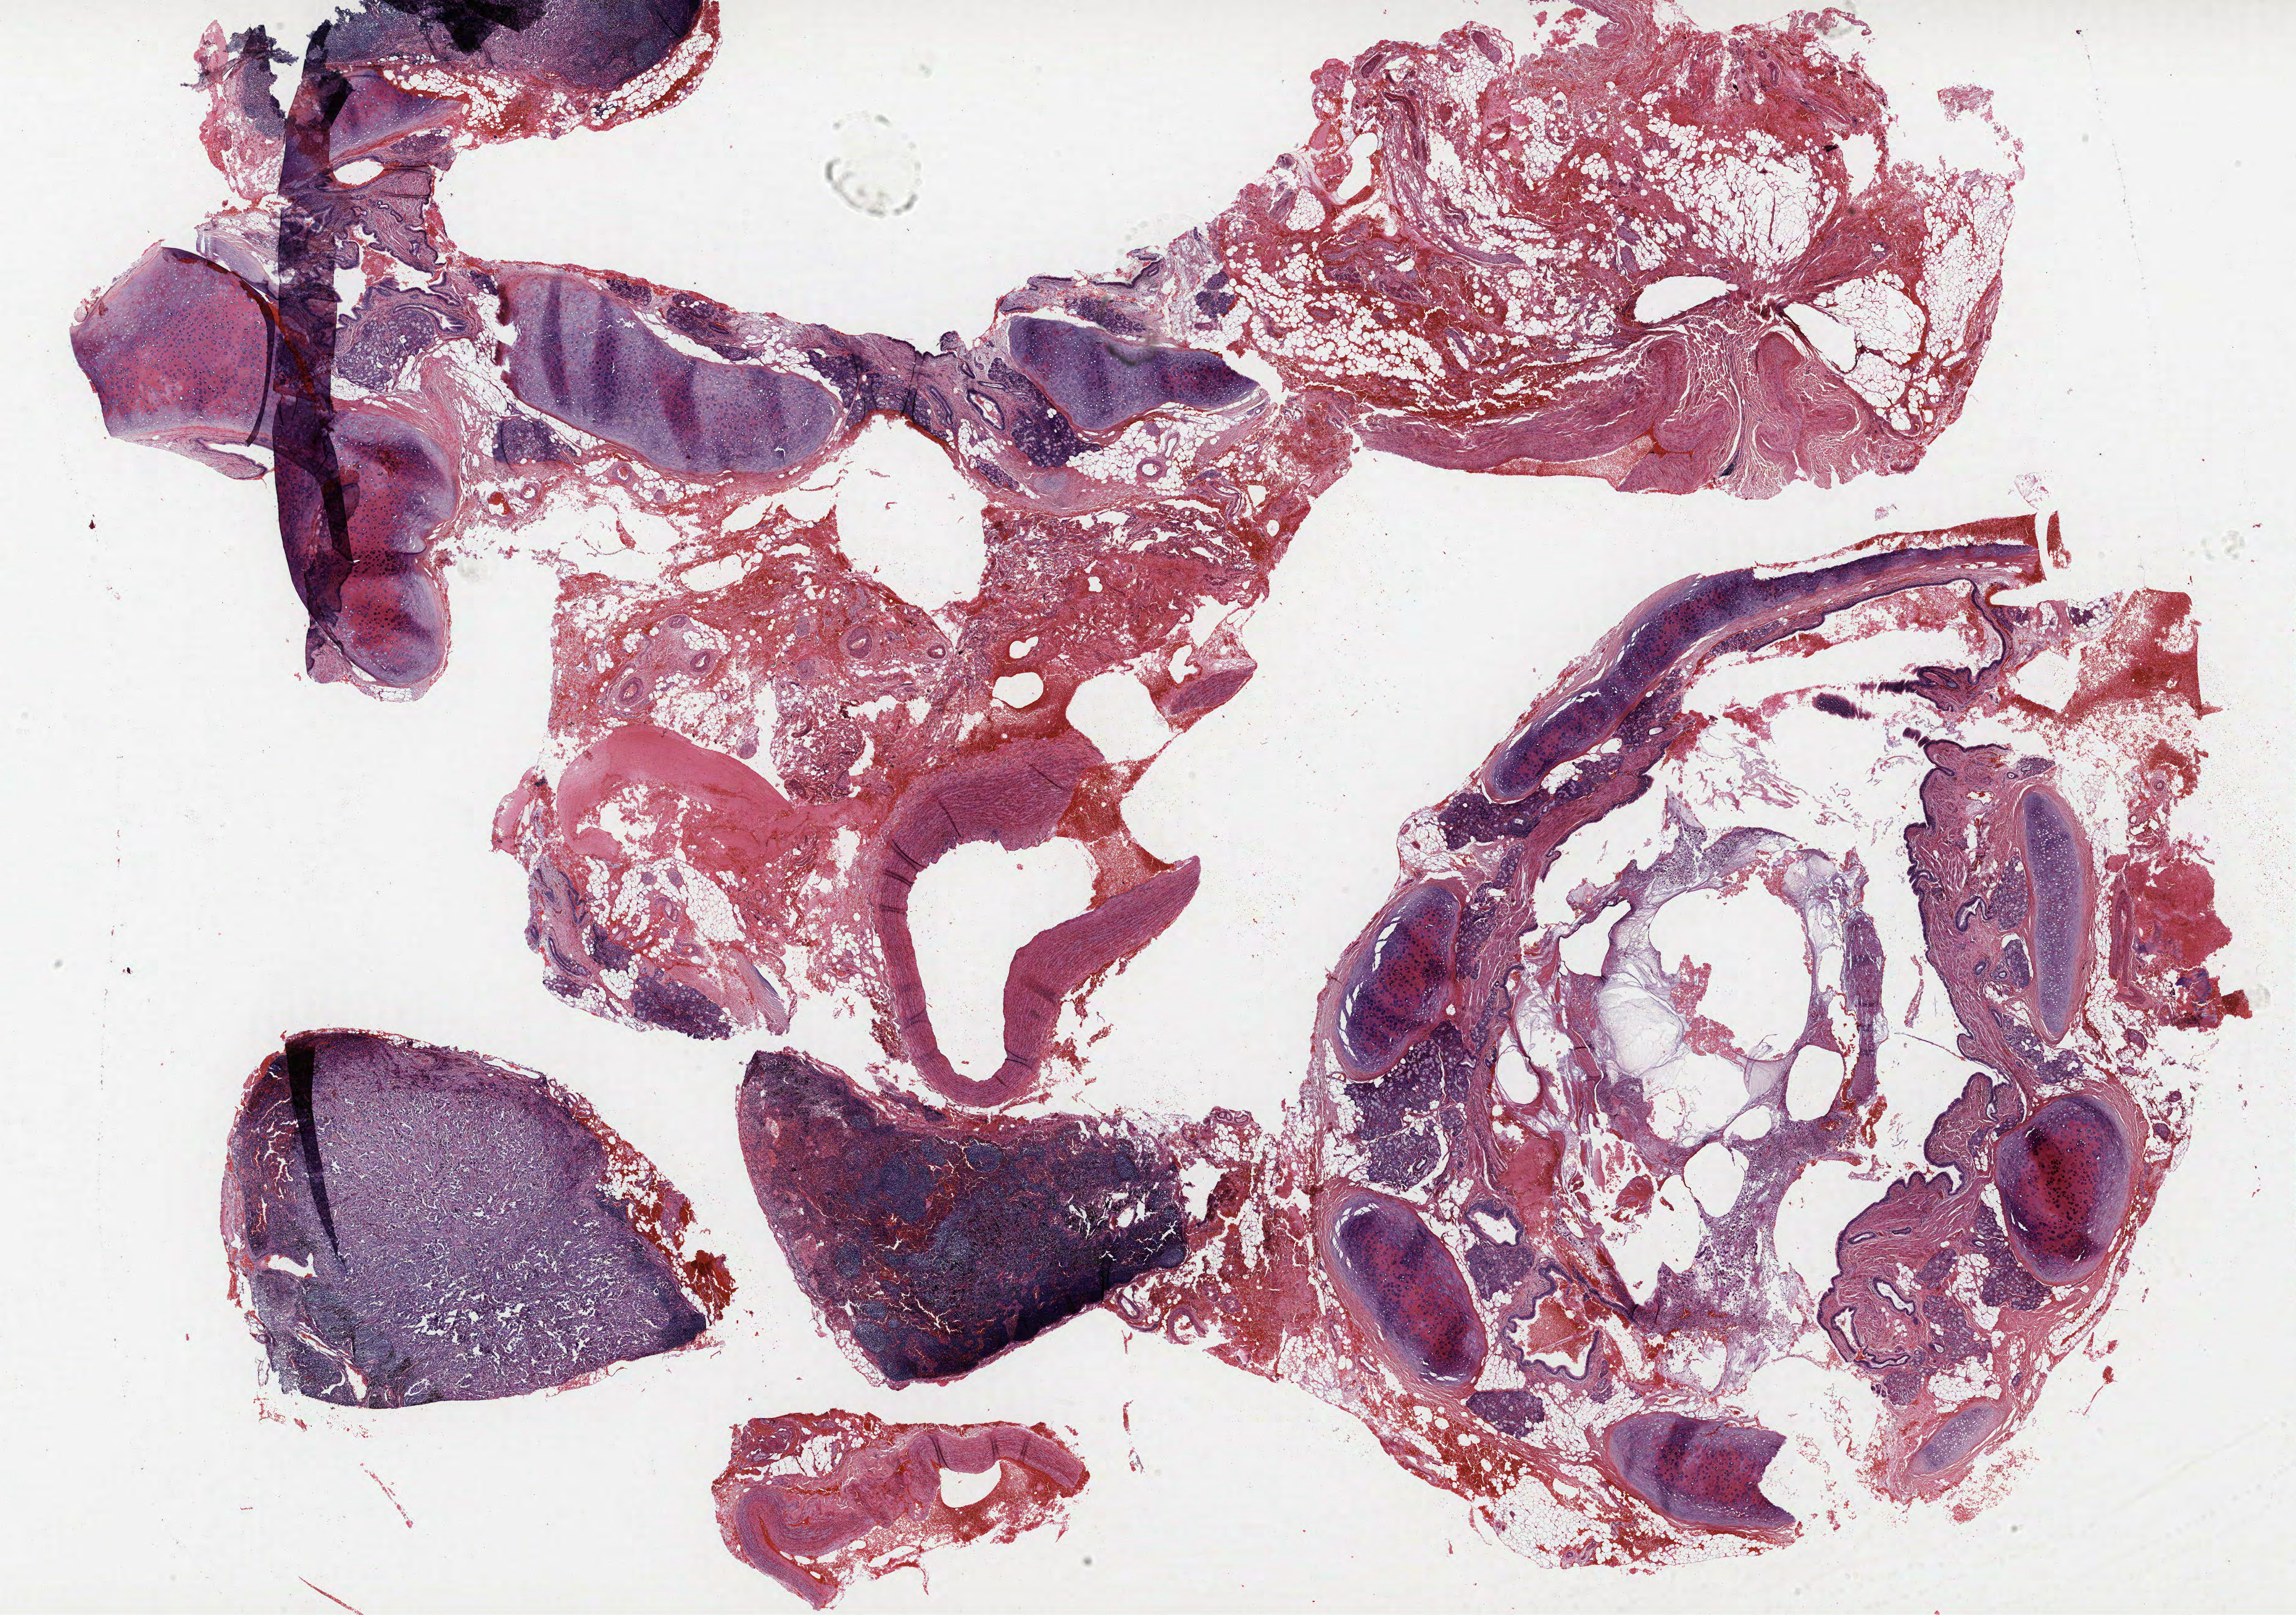
Whole-slide histology image, Hematoxylin and eosin (H&E) stained, whole scanned area (about 29.8 x 20.9 mm, from a 40x scan) shown as a low-resolution overview. FFPE section. Lung tissue. Male, age 64 at enrolment. Grade: poorly differentiated (G3).
Stage (AJCC 6th edition): IIA. Primary tumour location (clinical record): left upper lobe. Participant's lung-cancer diagnosis: Adenocarcinoma, NOS. Tumour size (pathology): 9 mm.